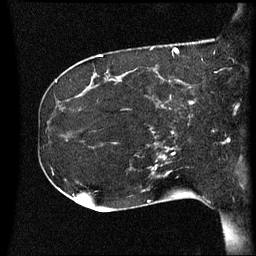
Breast MRI (dynamic contrast-enhanced), one sagittal slice; position 19 of 60 along the scan axis; dynamic contrast-enhanced series, image 2 of 3 at this slice position (ordered by acquisition); 1.5 T; TE 4.2 ms, TR 8.4 ms; 2.2 mm slice thickness; 256 × 256 image matrix, field of view 220 × 220 mm. Patient: female, 41 years. Case-level facts recorded for this patient, not image findings: setting: breast cancer imaged before/during neoadjuvant chemotherapy; receptor status: HER2-positive.
Outlined on this slice (semi-automatically segmented with operator editing):
- analysis volume of interest (the breast-tissue region the enhancement analysis was run in; not a lesion): bounding box (x1, y1, x2, y2) in pixels: (122, 80, 197, 119)
- tumour enhancement mask (voxels above the 70 % enhancement threshold inside the analysis volume of interest): (190, 102, 194, 105)